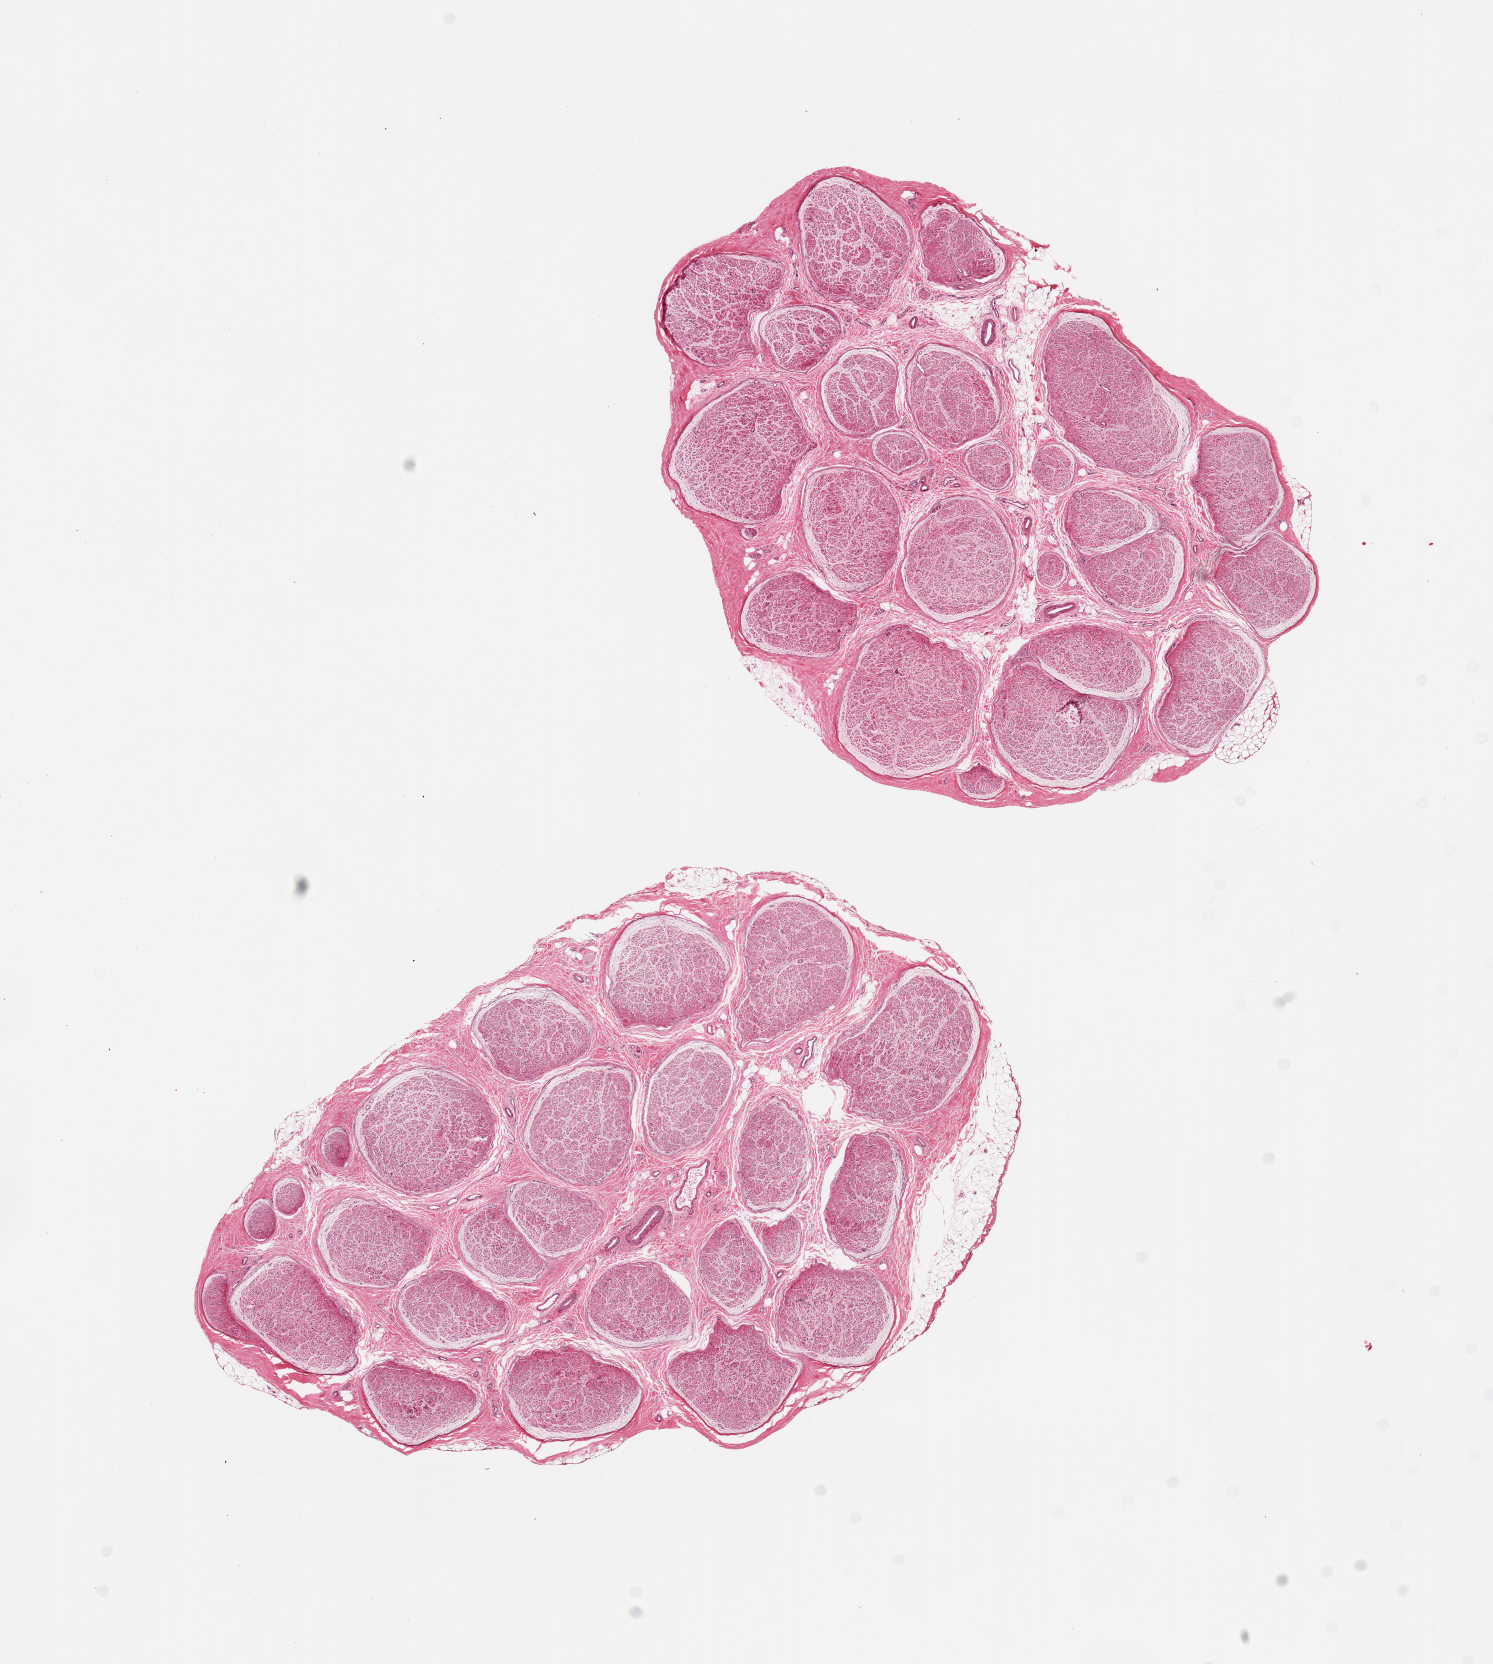
Hematoxylin and eosin (H&E) whole-slide image — shown as a low-resolution overview of the whole scanned area (about 11.8 x 13.2 mm, acquisition: 20x scan). PAXgene-fixed paraffin-embedded (PFPE) section. Target tissue: tibial nerve. Tissue donor sample. Donor: male.
Reviewer comment on this tissue sample: 2 pieces; minimal attached fat.